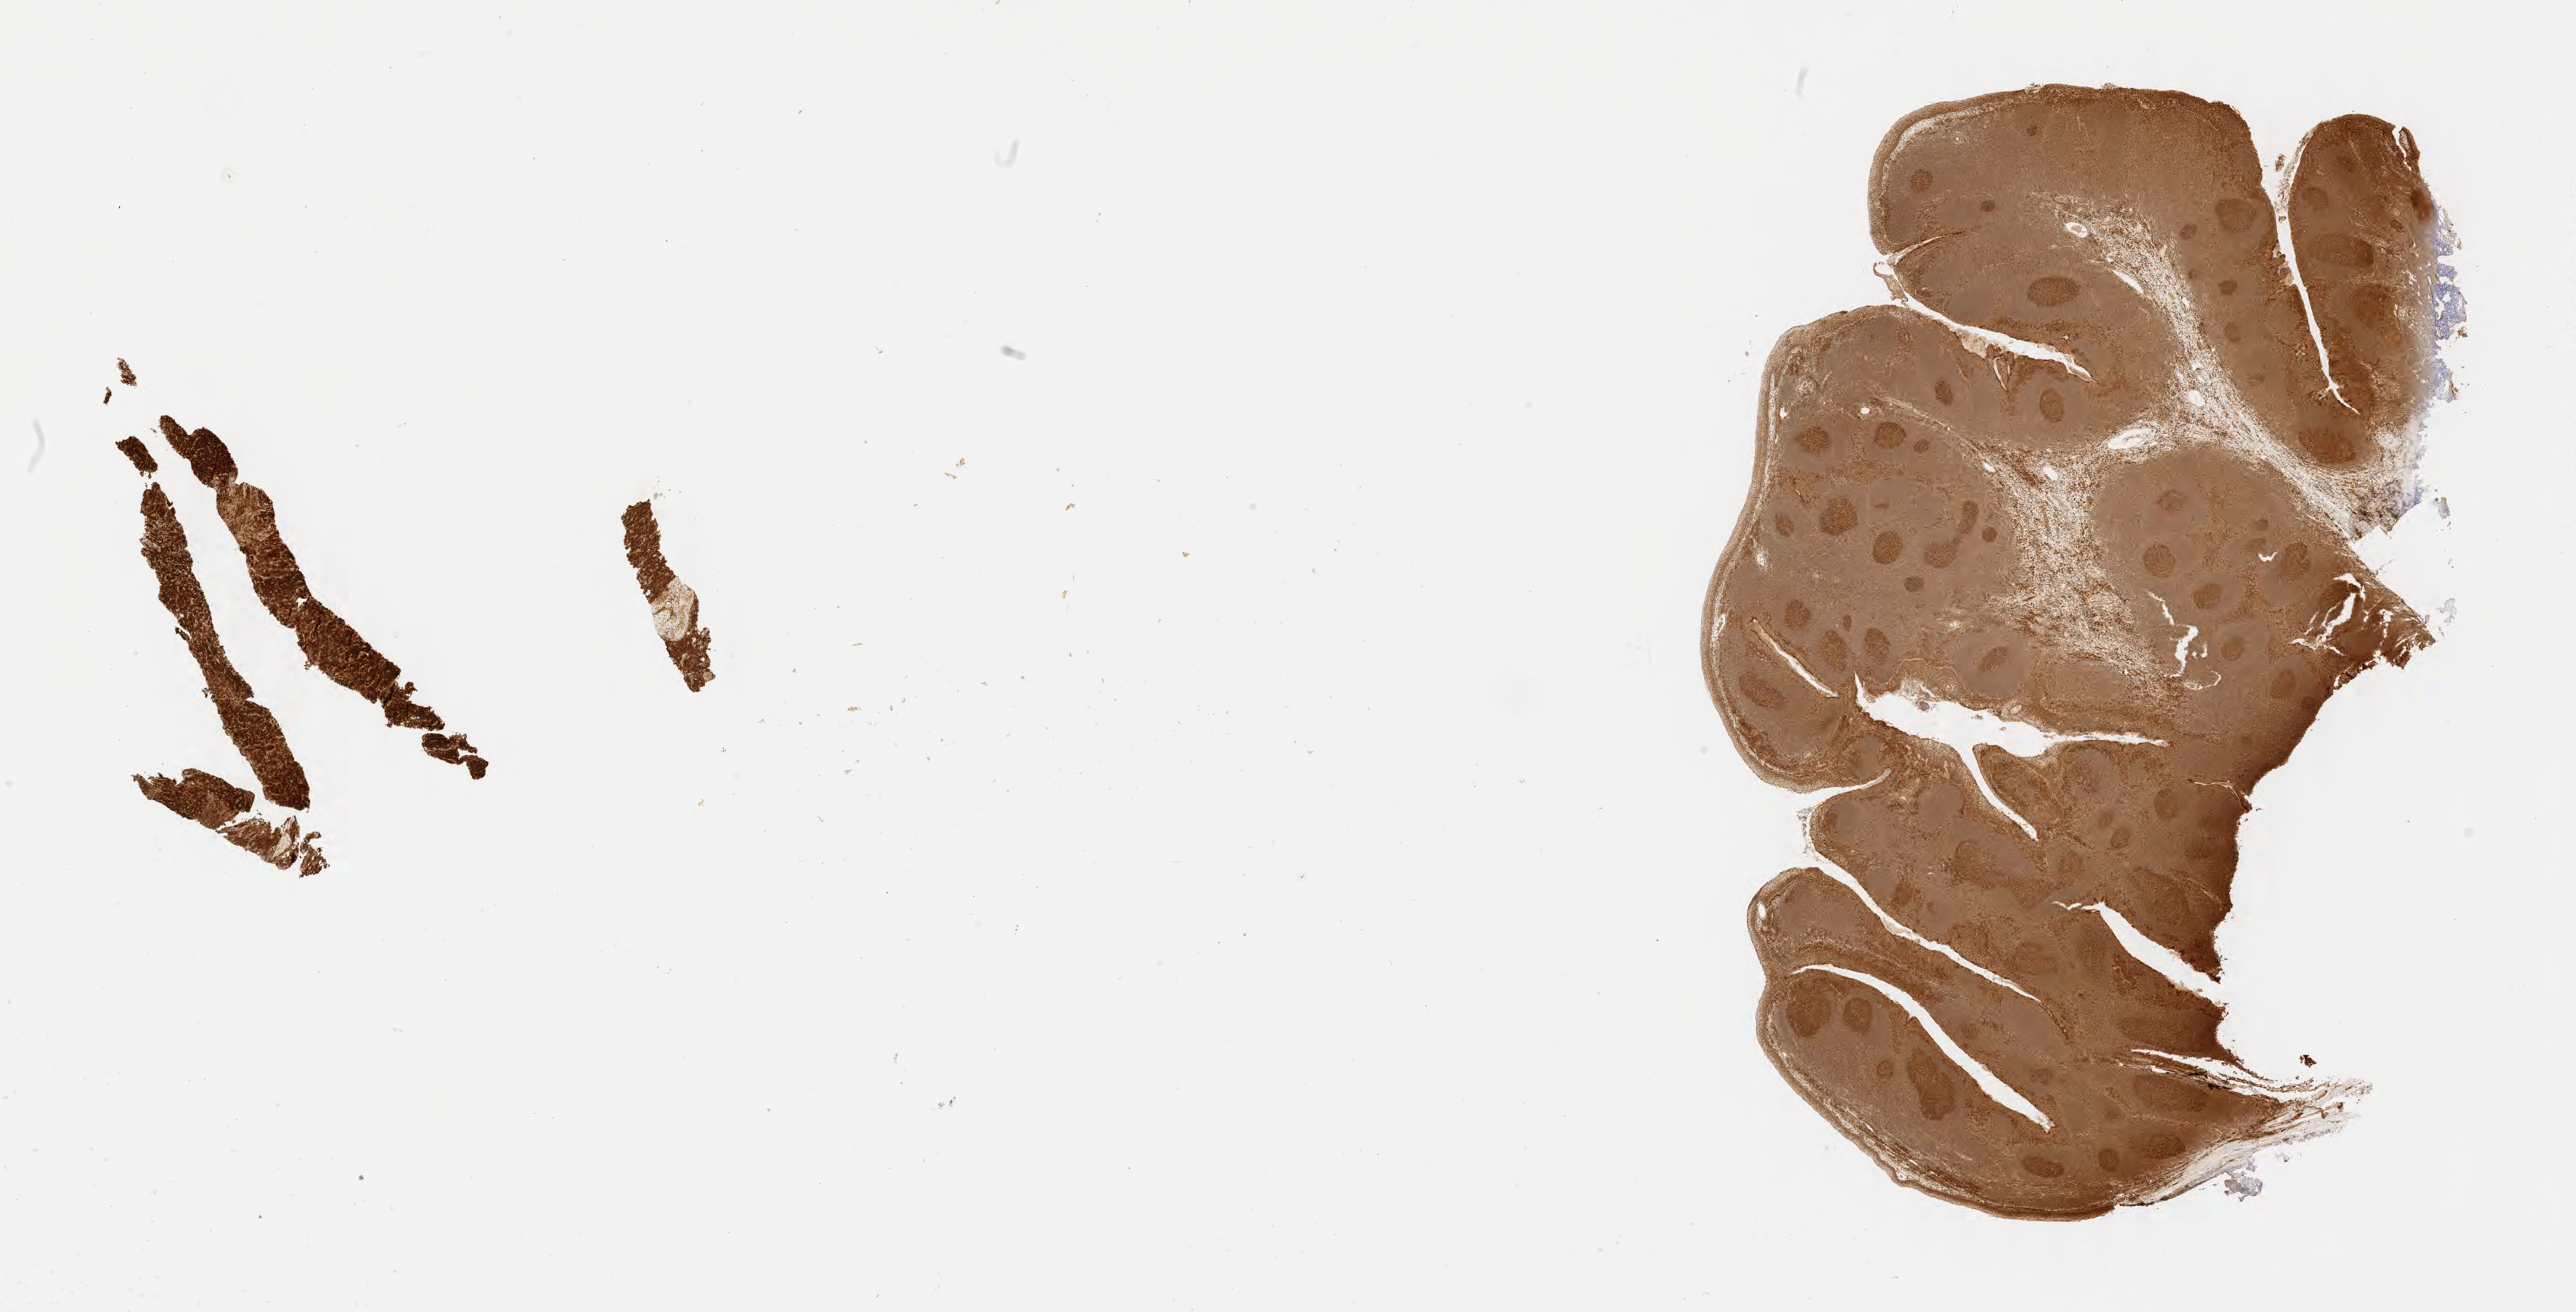
IHC for BCL6, whole-slide image, whole scanned area (about 28.7 x 14.6 mm) shown as a low-resolution overview, tumor tissue. Patient male; 13 years old.
Histologic diagnosis: Diffuse large B-cell lymphoma, NOS.